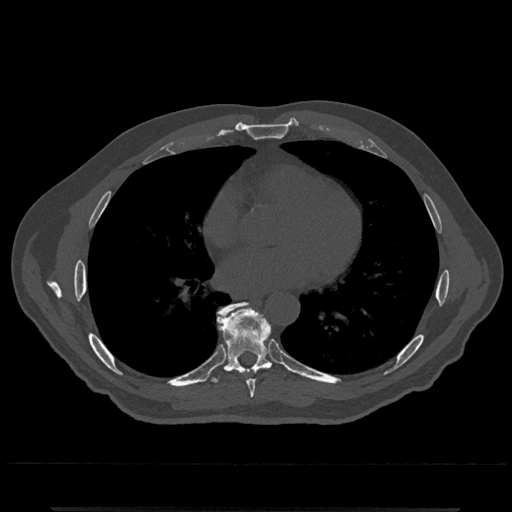
CT including the spine, one axial slice. Reconstruction kernel Br40s/3. Bone window (W 1800 / L 400 HU). 512 × 512 image matrix, field of view 393 × 393 mm. Patient: male, 67 years. Case-level facts recorded for this patient, not image findings: primary cancer: prostate.
Annotated regions visible in this slice (semi-automatically segmented with operator editing):
- T7 vertebra: bounding box <247,368,263,398> (left, top, right, bottom; pixels)
- T8 vertebra: <208,302,273,385>